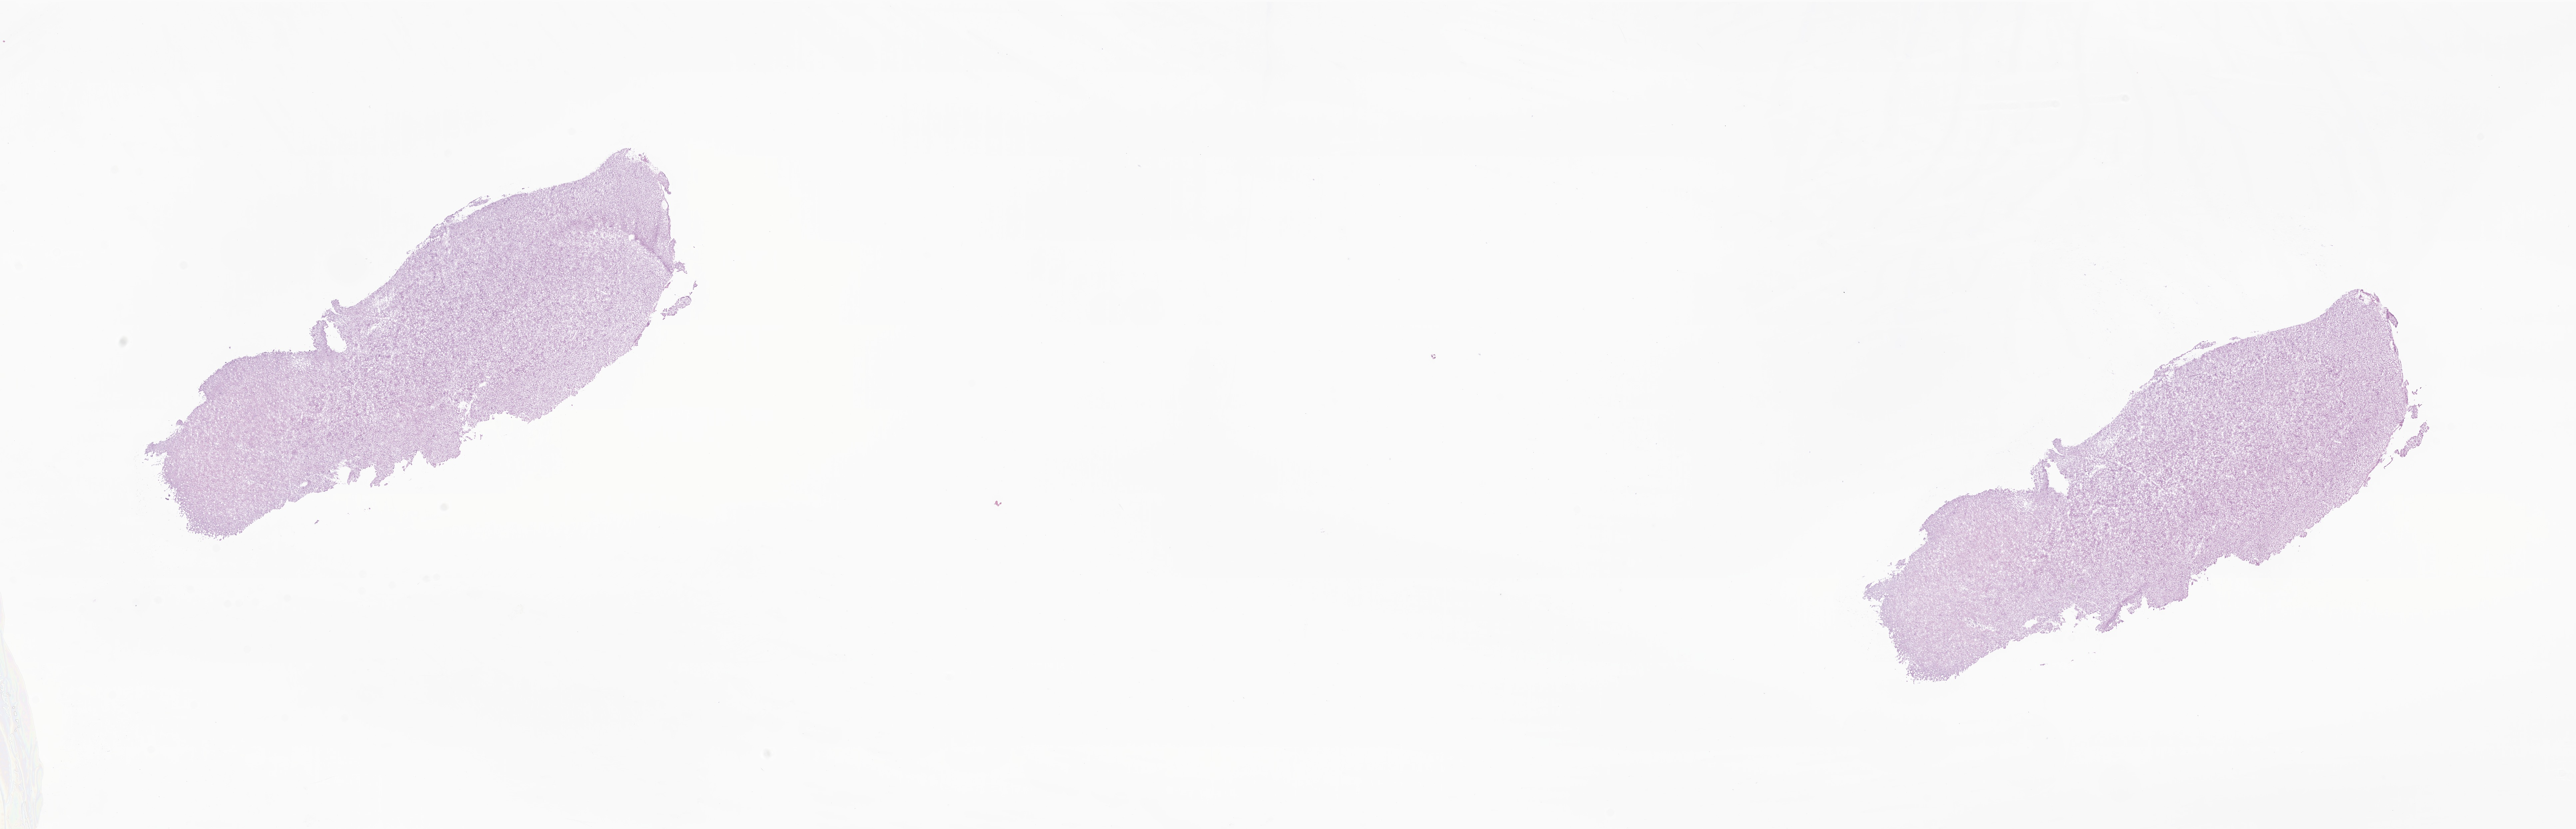
Hematoxylin and eosin (H&E) whole-slide image of tumor tissue from the temporal lobe, low-resolution overview of the scanned area, about 32.6 x 10.5 mm. Cryosection (OCT / tissue freezing medium). Male patient, age 104 months.
Diagnosis (ICD-O-3 morphology term): Glioma, malignant.